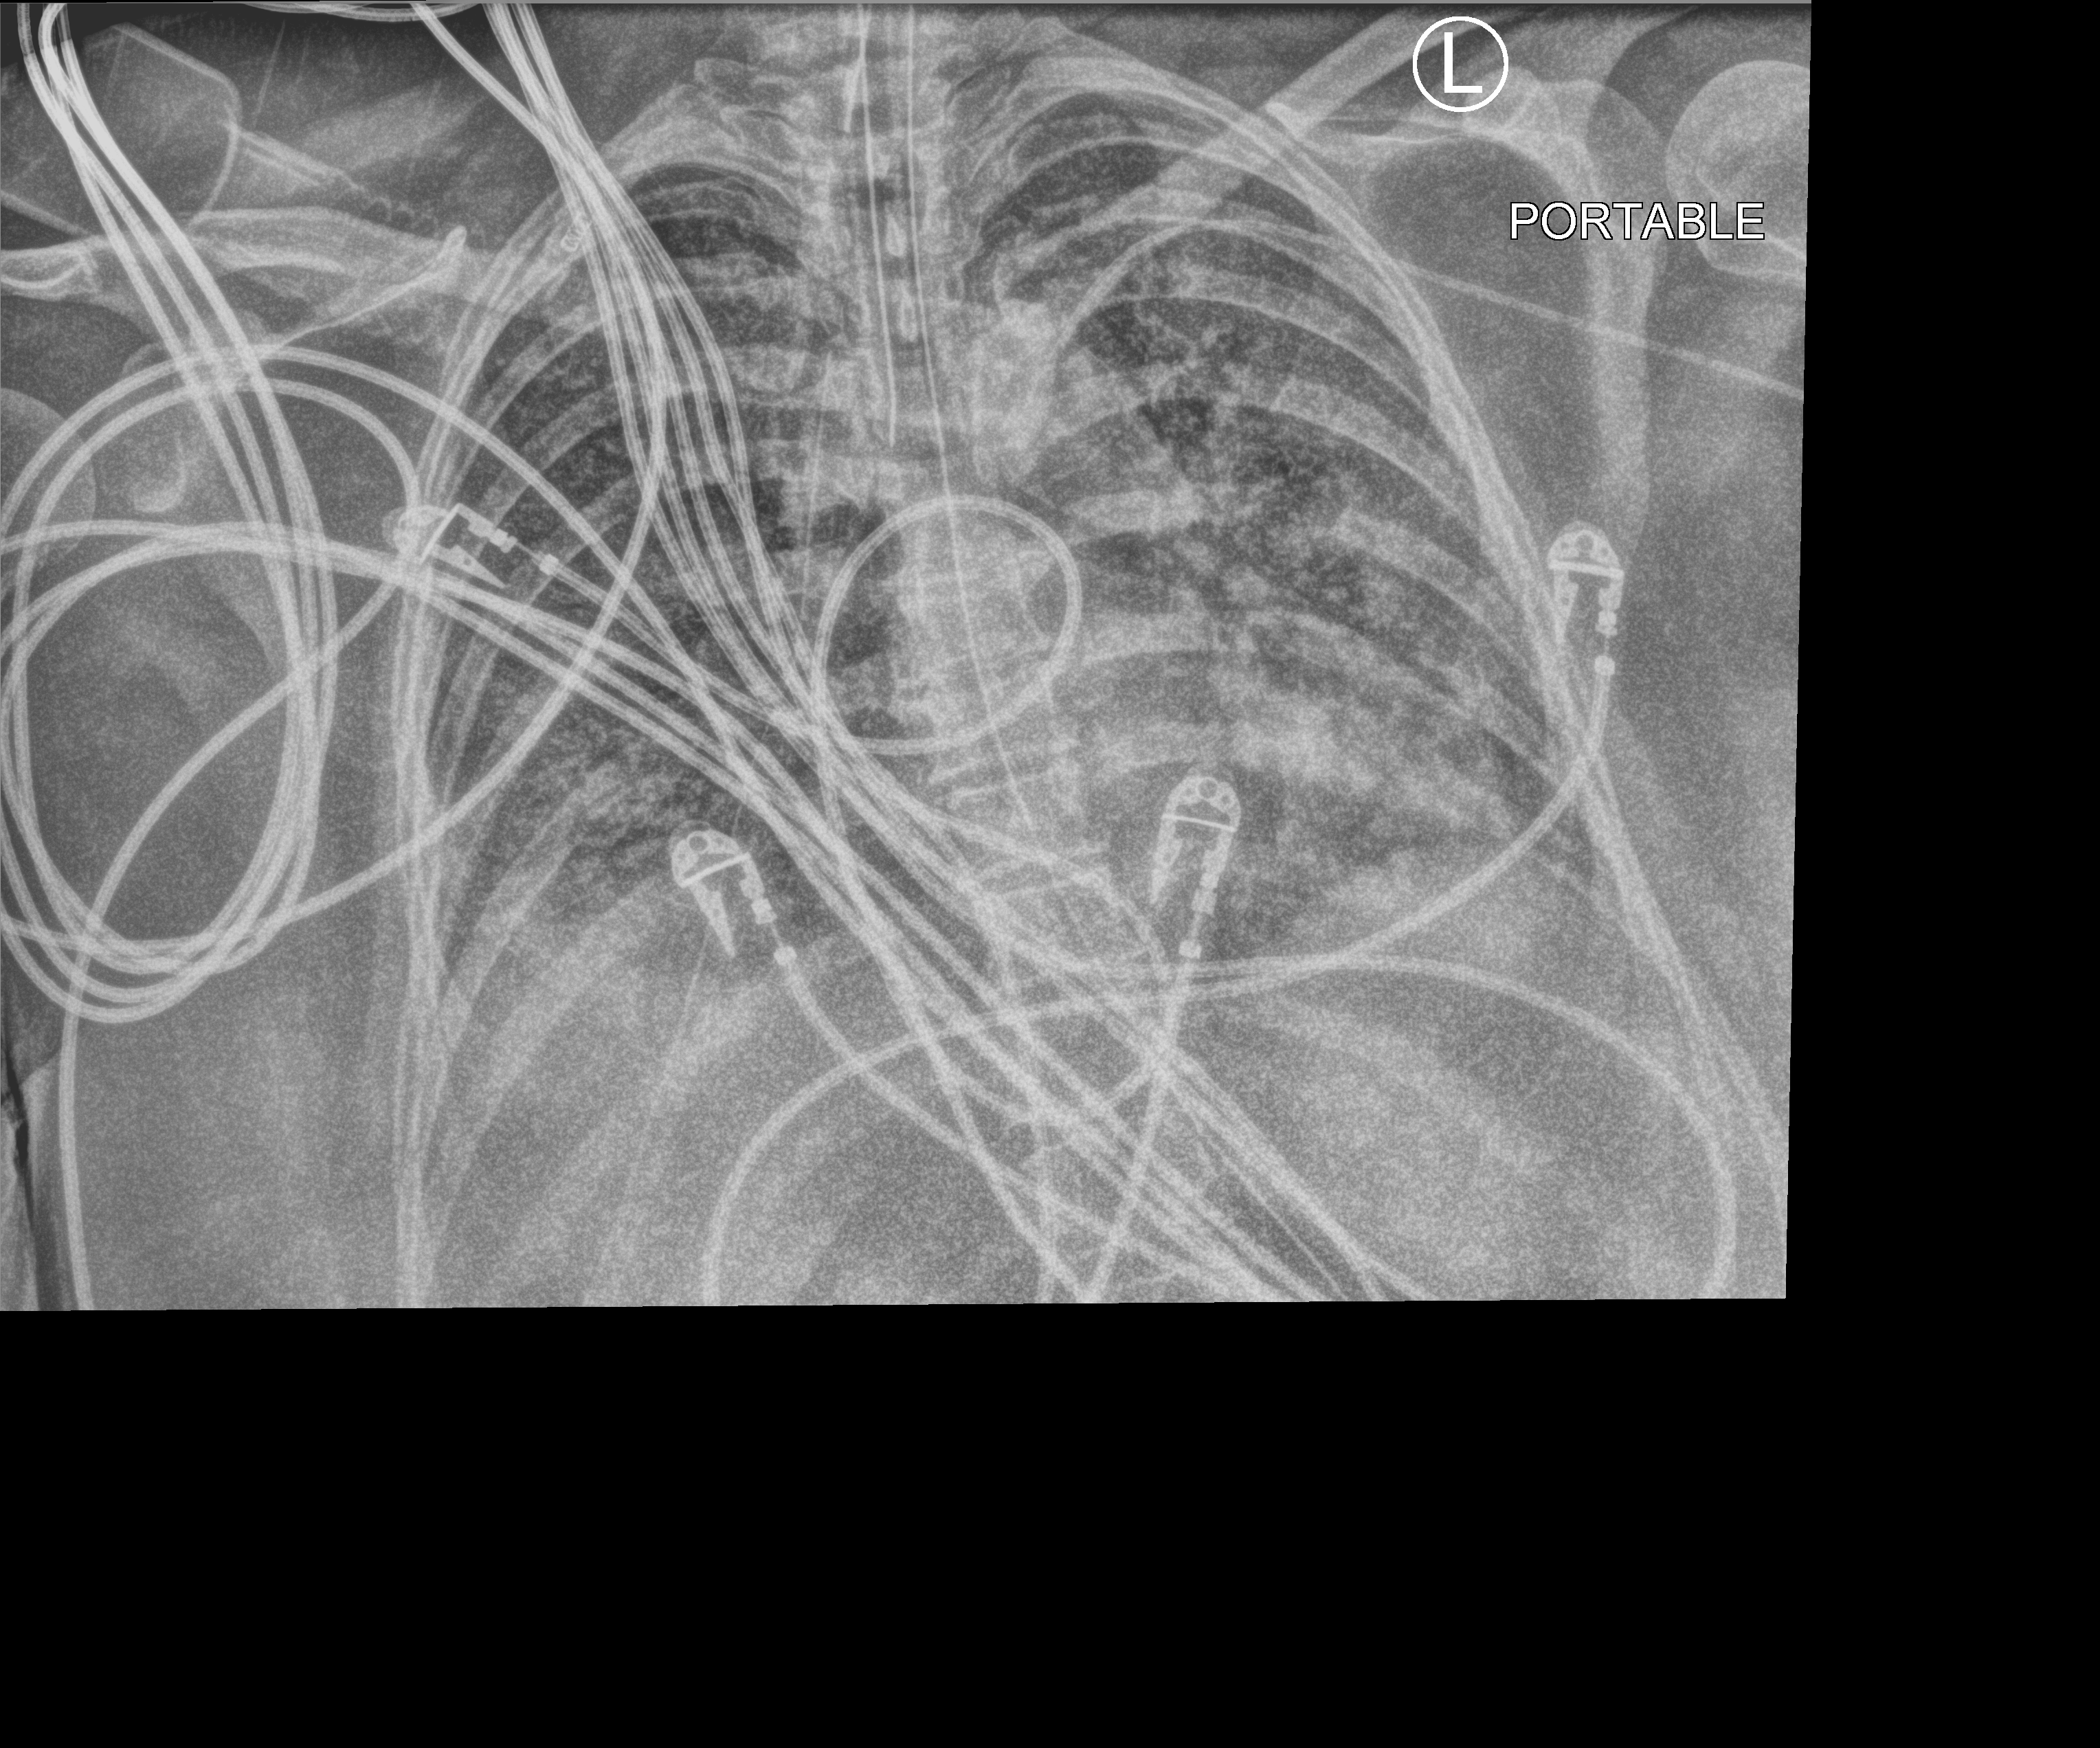
Bedside chest radiograph (computed radiography); anteroposterior (AP) projection. Patient hospitalised with COVID-19; female, aged 18–59 years.
Hospital-stay facts (about this admission, not read from this image; timing relative to this image not recorded):
- mechanically ventilated during this hospital stay: yes
- hypertension (admission record): yes
- admitted to intensive care during this hospital stay: yes